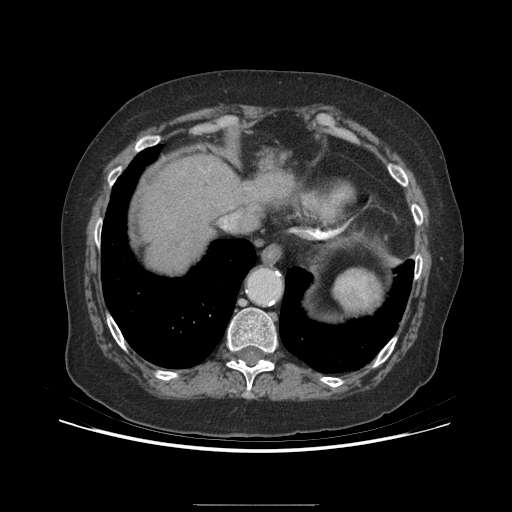
Contrast-enhanced abdominal CT (liver protocol), one axial slice. Slice 178 of 192 in the series (ordered by position). Soft-tissue window (W 400 / L 40 HU). 2.5 mm slice thickness. 512 × 512 image matrix, field of view 400 × 400 mm. From the clinical record (not read from this slice): diagnosis: hepatocellular carcinoma (patient treated with transarterial chemoembolisation; whether this scan precedes or follows treatment is not stated here); TNM stage (as recorded): Stage-I; Child-Pugh class: A; tumour differentiation: moderately differentiated; tumour nodularity: uninodular.
Annotated regions visible in this slice (semi-automatic segmentation, software-assisted and operator-edited):
- abdominal aorta: bounding box <249,269,280,303> (left, top, right, bottom; pixels)
- liver parenchyma outside the tumour (the mass and vessels are separate outlines, so this box may not span the whole liver): <140,154,290,270>